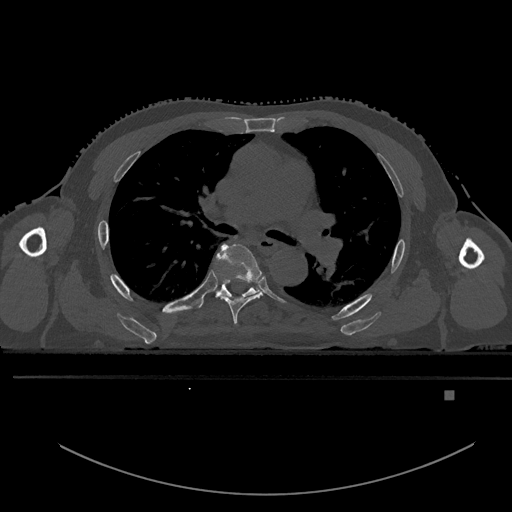
CT including the spine, one axial slice; bone window (W 1800 / L 400 HU); 0.5 mm slice thickness; 512 × 512 image matrix, field of view 456 × 456 mm. Male patient, age 82 years. From the clinical record (not read from this slice): primary cancer: prostate.
Structures marked on this image (semi-automatically segmented with operator editing):
- T5 vertebra: bounding box <214,244,263,325> (left, top, right, bottom; pixels)
- T6 vertebra: <198,278,259,308>